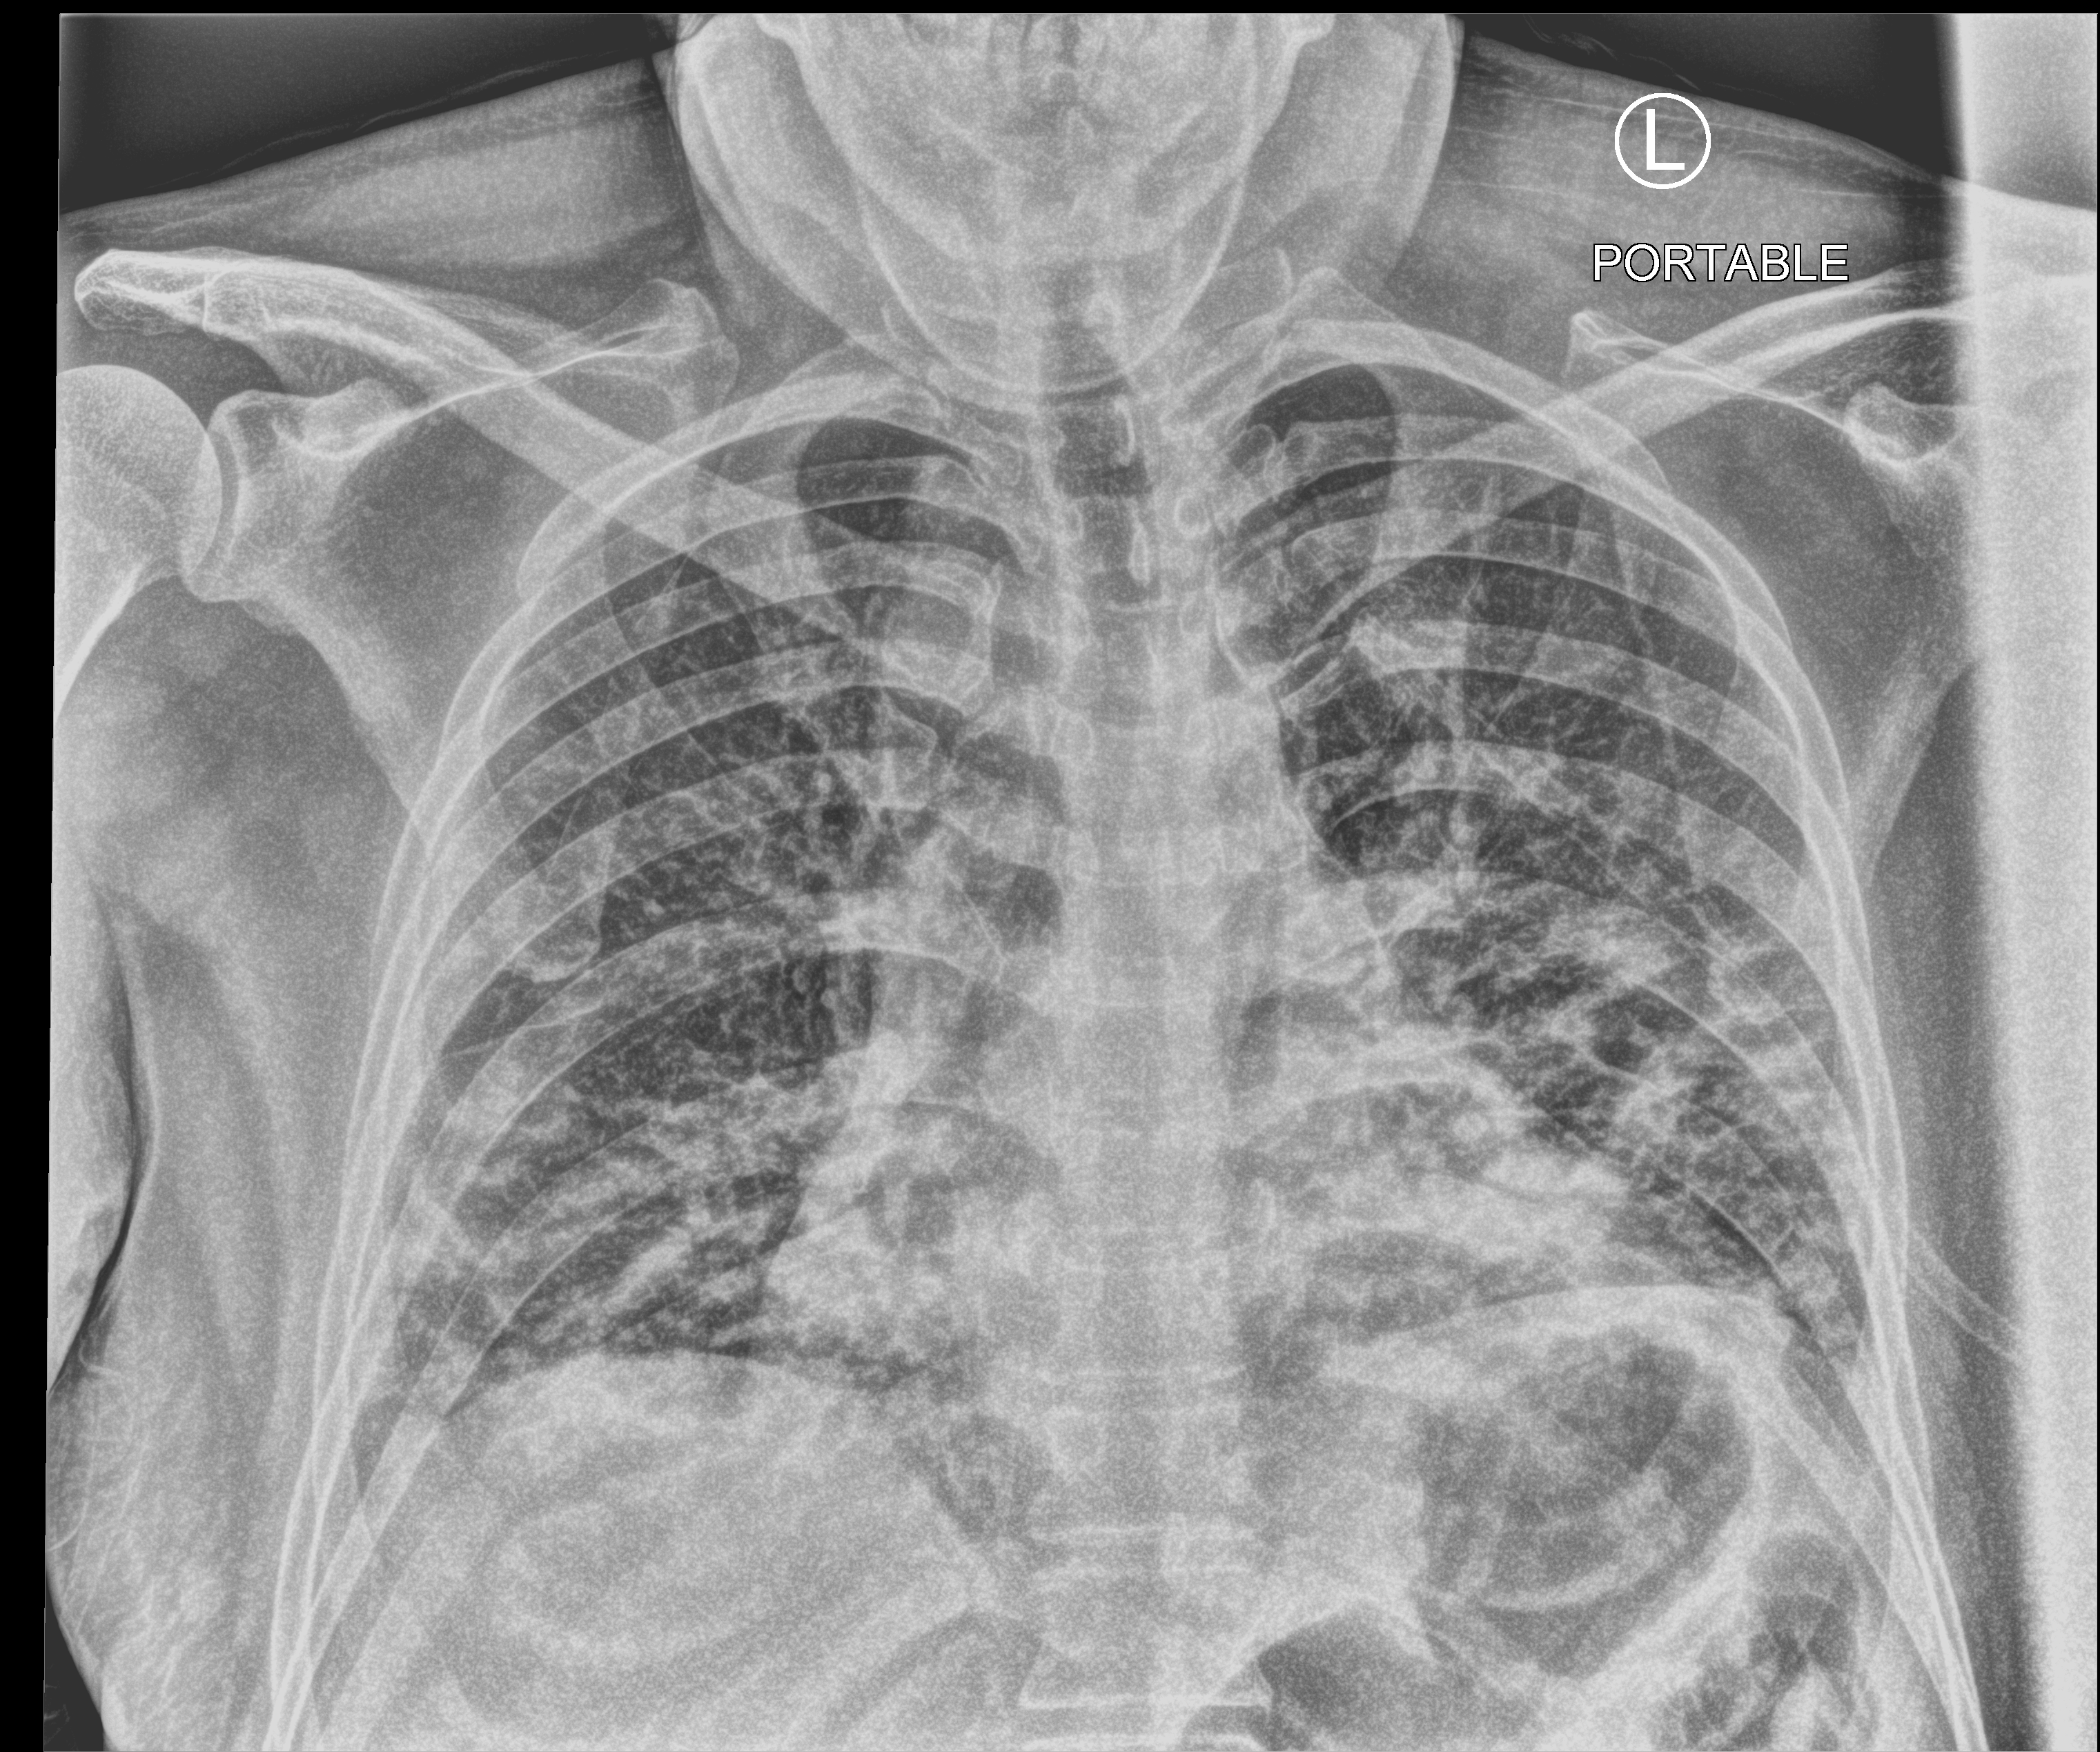
Chest X-ray (portable), anteroposterior (AP) projection. Patient hospitalised with COVID-19; male, aged 18–59 years.
Hospital-stay facts (about this admission, not read from this image; timing relative to this image not recorded): diabetes (admission record): yes; length of hospital stay: 15 days.